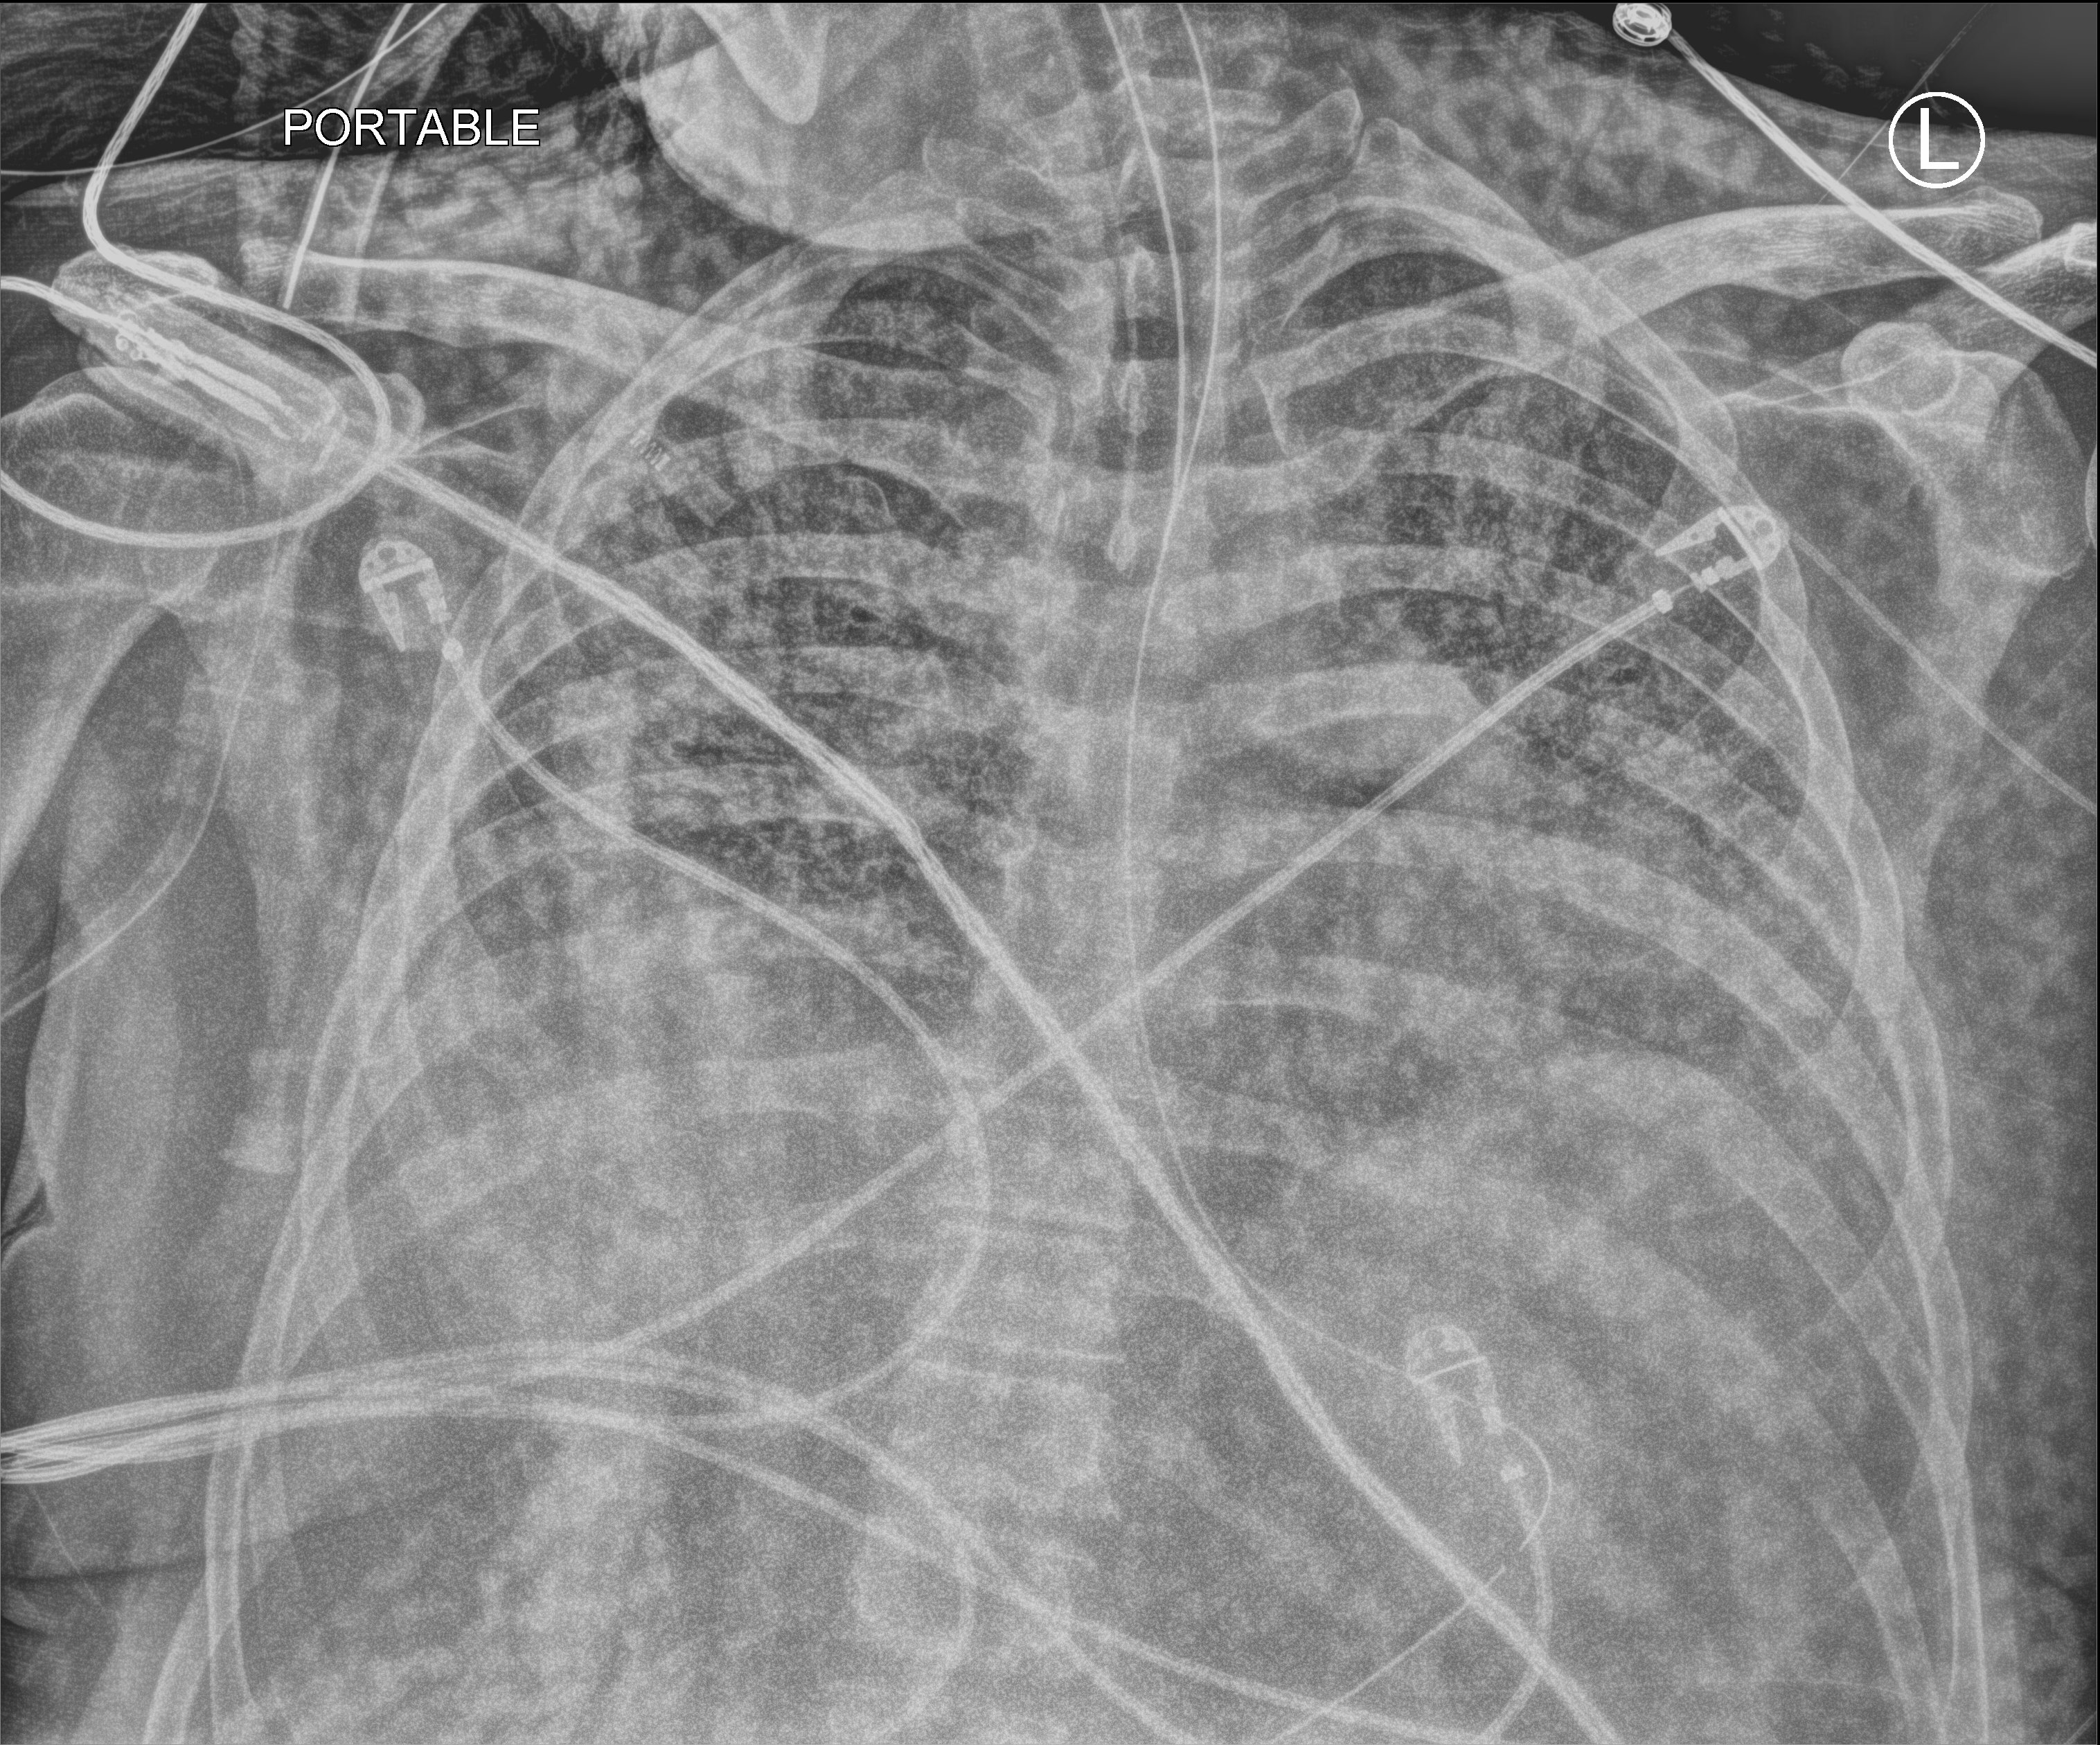
Chest X-ray (portable). Male patient hospitalised with COVID-19, age 18–59 years.
Admission-level facts for this patient (not findings on this image; timing relative to this image not recorded): chronic kidney disease (admission record): no; mechanically ventilated during this hospital stay: yes; admitted to intensive care during this hospital stay: yes.